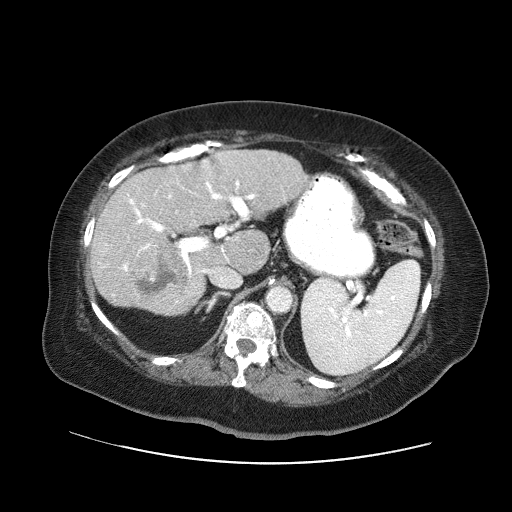
Contrast-enhanced abdominal CT (liver protocol), one axial slice. Position 32 of 71 along the scan axis. 120 kVp. Soft-tissue window (W 400 / L 40 HU). 2.5 mm slice thickness. 512 × 512 image matrix, field of view 400 × 400 mm. From the clinical record (not read from this slice): diagnosis: hepatocellular carcinoma (patient treated with transarterial chemoembolisation; whether this scan precedes or follows treatment is not stated here); TNM stage (as recorded): Stage-II; Child-Pugh class: A; tumour differentiation: poorly differentiated; tumour nodularity: multinodular.
Outlined on this slice (semi-automatically segmented with operator editing):
- liver parenchyma outside the tumour (the mass and vessels are separate outlines, so this box may not span the whole liver): bounding box <90,150,306,314> (left, top, right, bottom; pixels)
- mass: <134,244,189,296>
- liver vessels: <105,154,255,276>